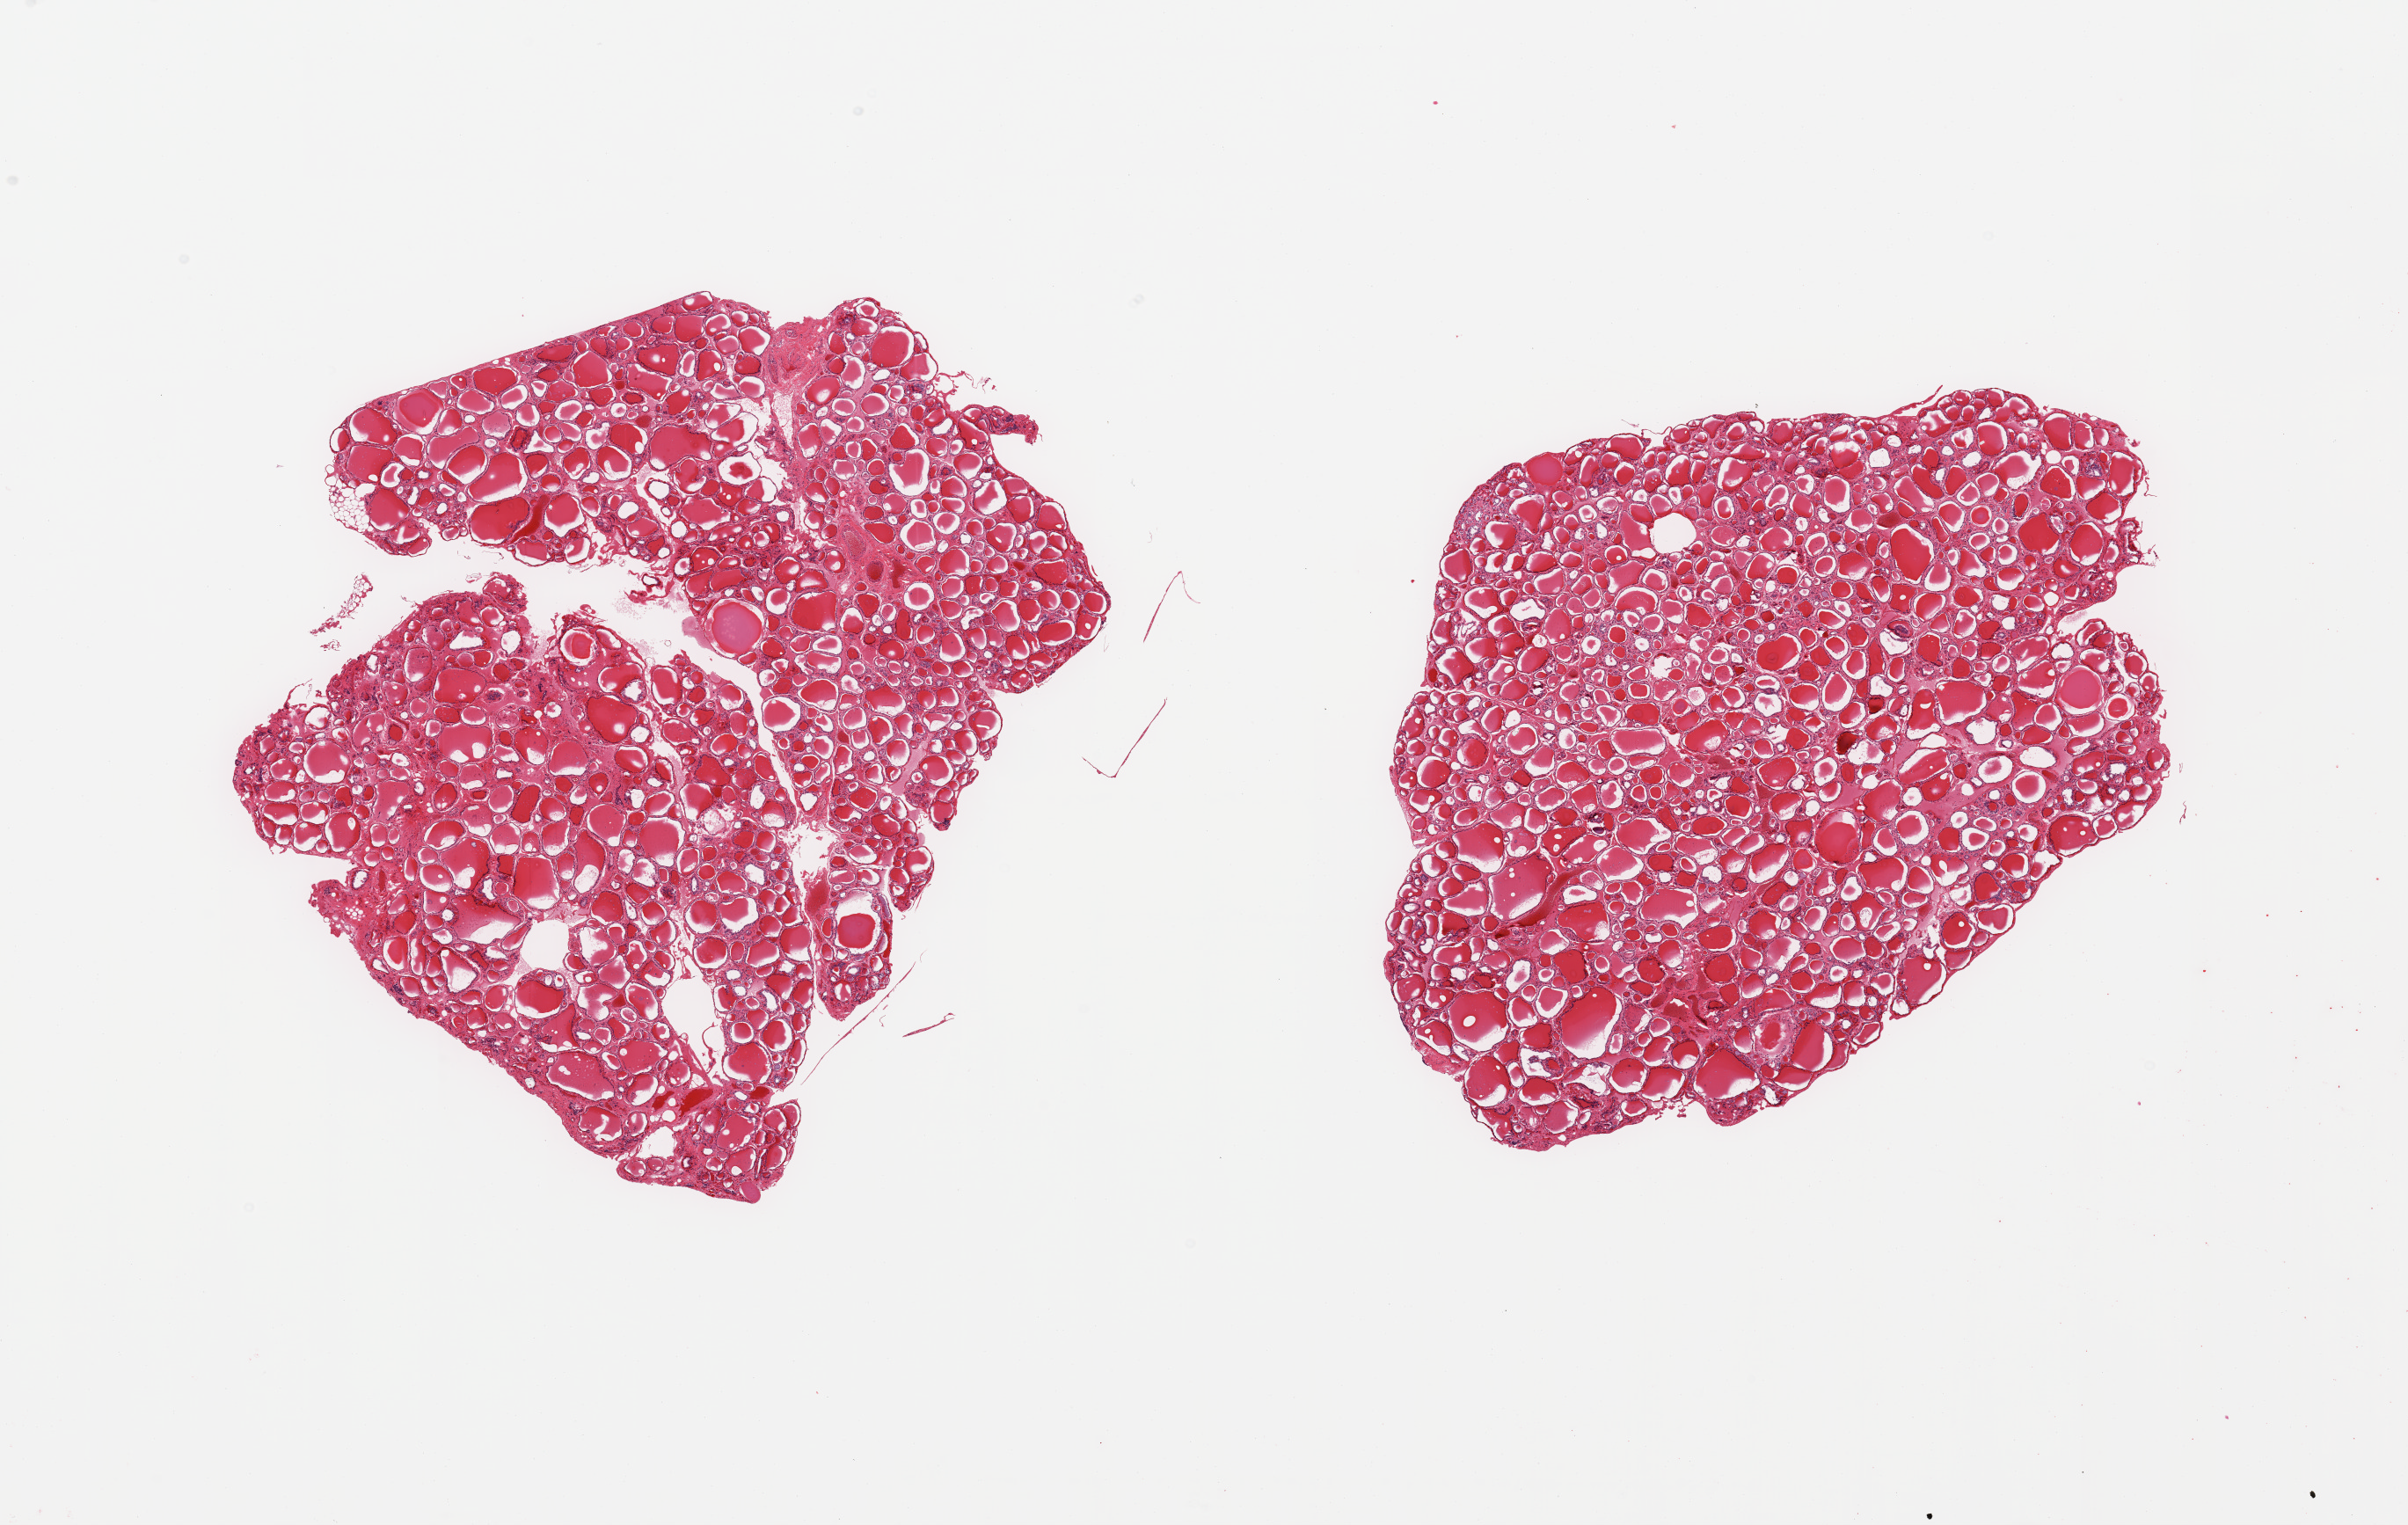
Digitized H&E-stained section, brightfield, shown as a low-resolution overview of the whole scanned area (about 21.7 x 13.7 mm). PAXgene-fixed paraffin-embedded (PFPE) section. Sampled site (target tissue): thyroid. Donor tissue sample.
Review note (as recorded): 2 pieces; no llesions.